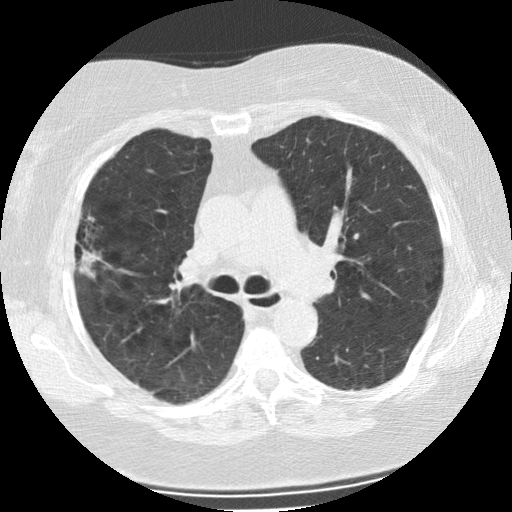
Low-dose screening chest CT, one axial slice. Slice 146 of 225 in the series (ordered by position). Reconstruction kernel STANDARD. 120 kVp. Lung window (W 1500 / L -600 HU). 2.5 mm slice thickness. 512 × 512 image matrix, field of view 320 × 320 mm.
Annotated regions visible in this slice (manually delineated by an expert):
- lesion 1 (tumor, upper lobe of right lung): box from (x=79, y=250) to (x=100, y=277) px